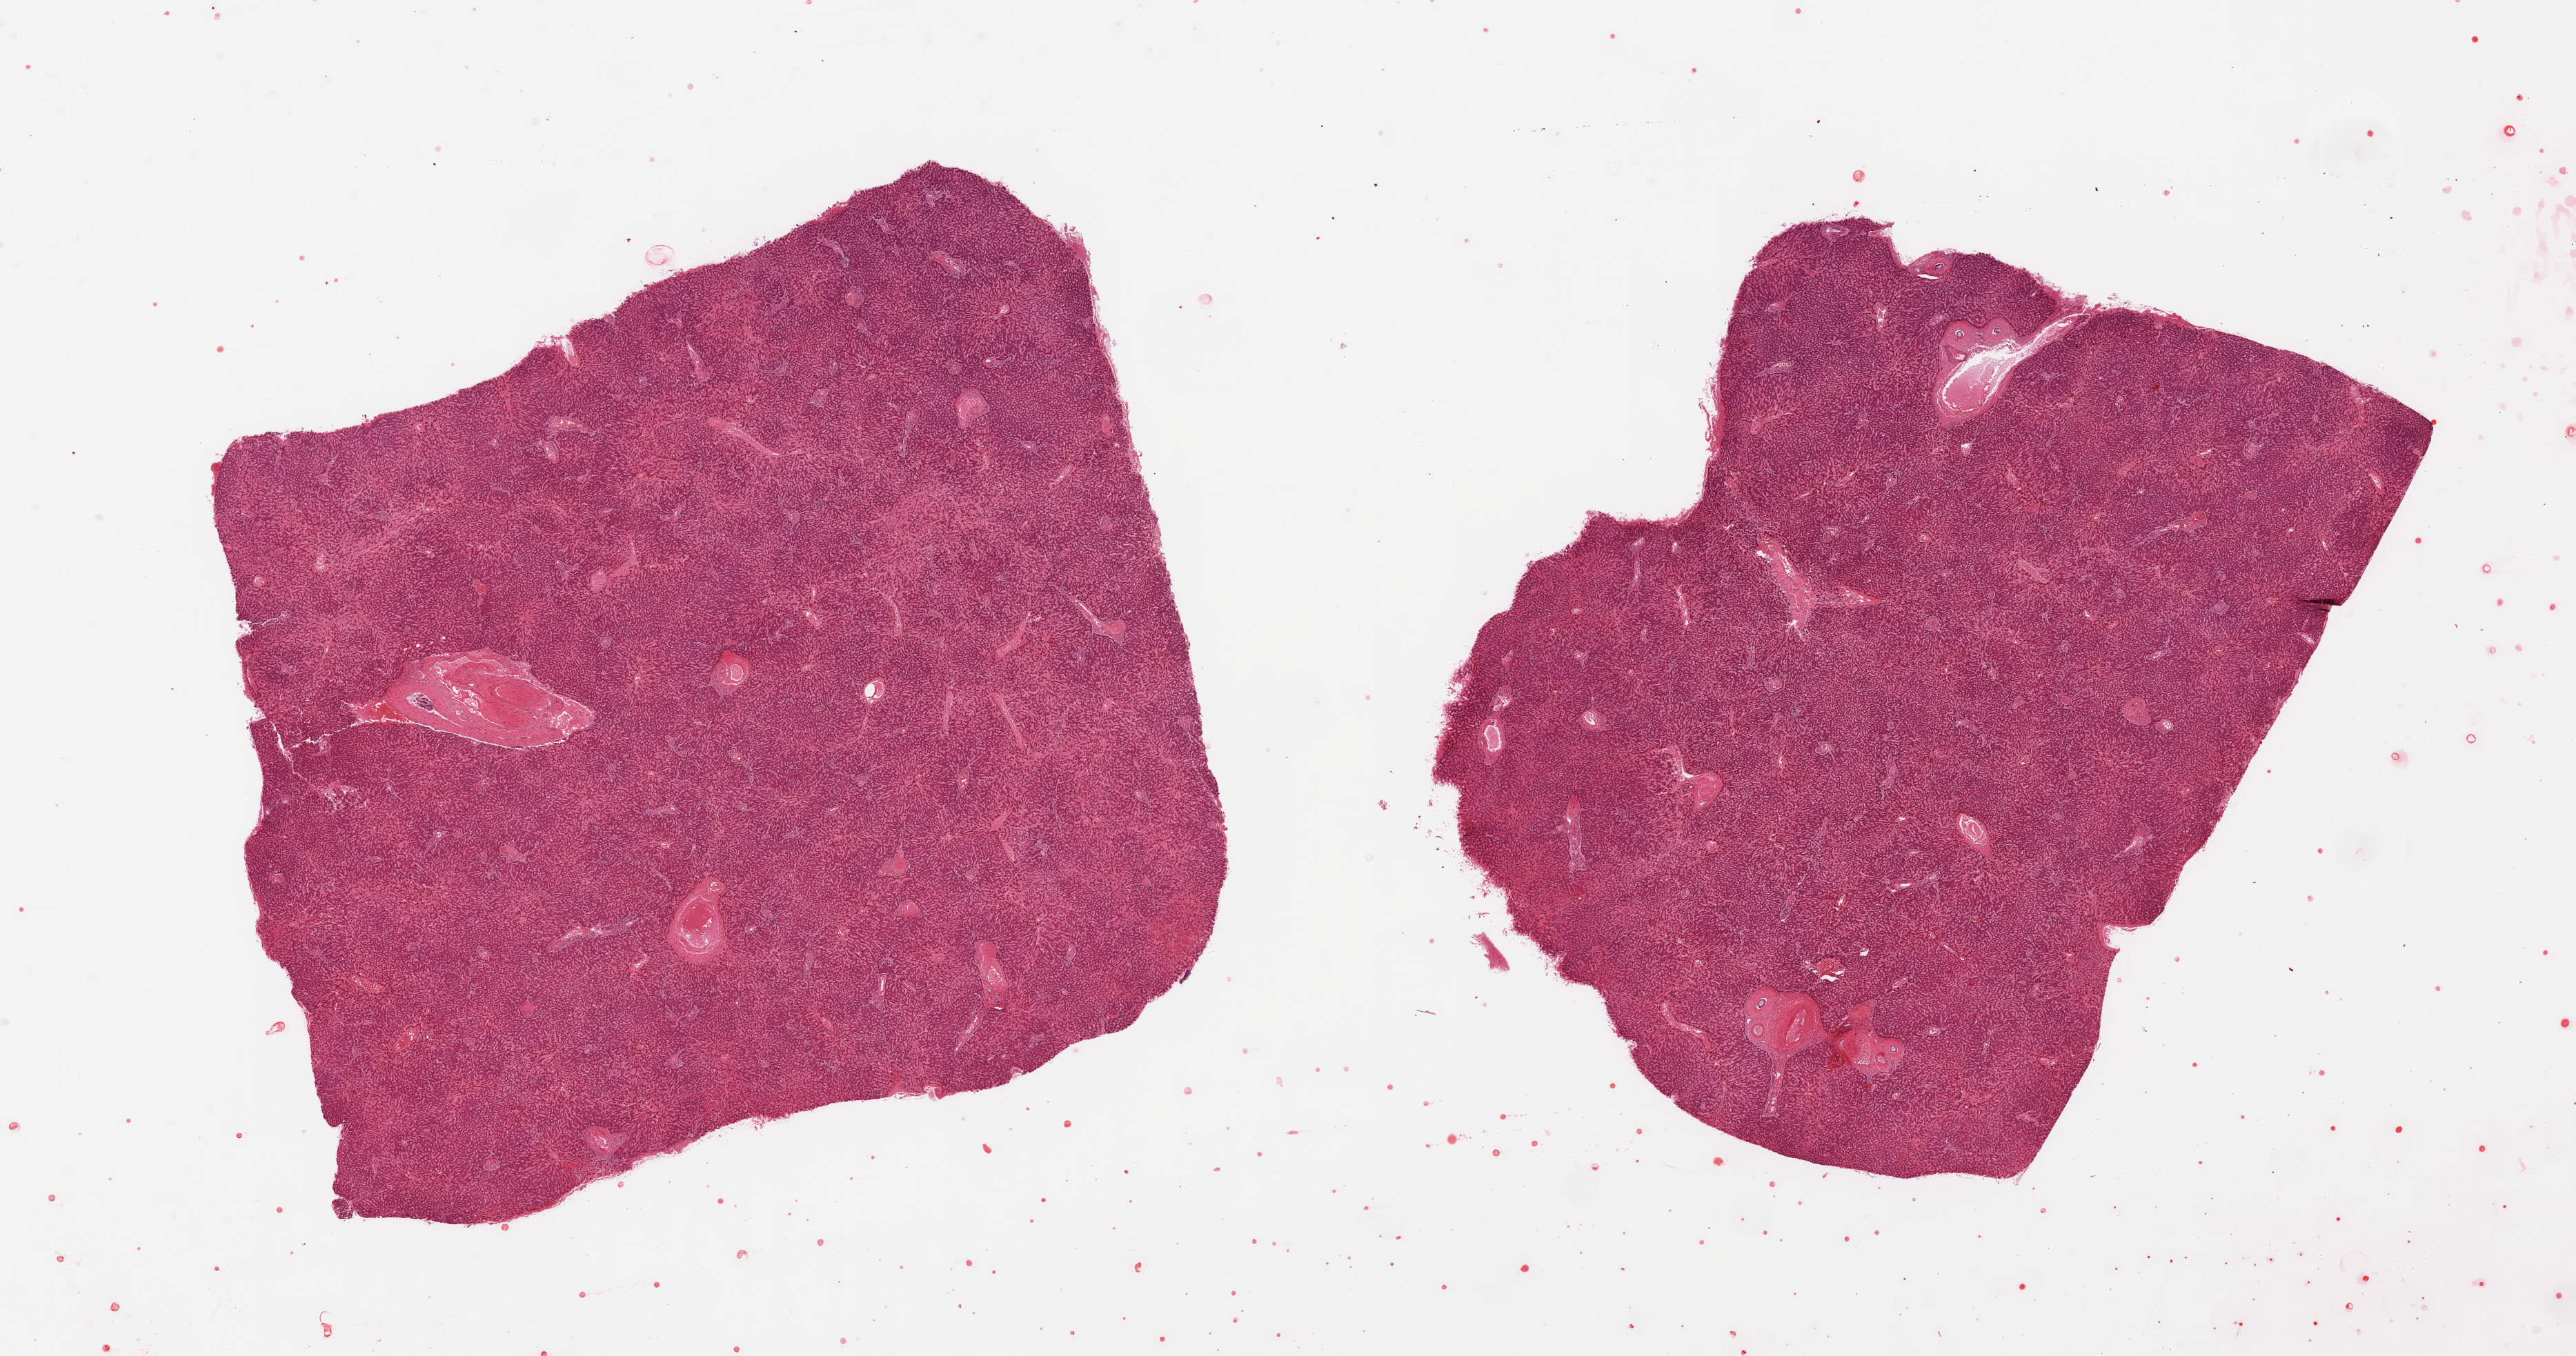
Haematoxylin and eosin whole-slide image, a low-resolution overview of the entire scanned area, about 29.5 x 15.5 mm (acquisition: 20x scan). PAXgene-fixed, paraffin-embedded tissue. Target tissue: liver. Donor tissue sample. Donor sex: female.
Reviewer comment on this tissue sample: 2 pieces; mild central congestion & atrophy.